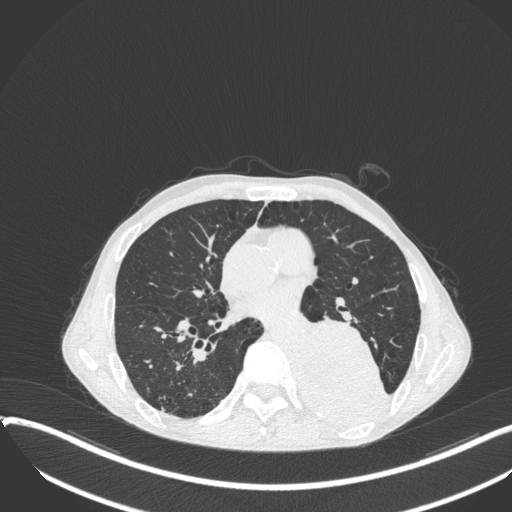
Chest CT, one axial slice. Slice 176 of 400 in the series (ordered by position). 120 kVp. Lung window (W 1500 / L -600 HU). 1 mm slice thickness. 512 × 512 image matrix, field of view 400 × 400 mm. Male patient, age 57 years. From the clinical record (not read from this slice): clinical TNM (as recorded): T4 N0 M0.
Outlined on this slice (rectangle marked by the reading radiologist):
- lung tumour (recorded histology: squamous cell carcinoma): bounding box [x1, y1, x2, y2] px = [301, 317, 390, 427]